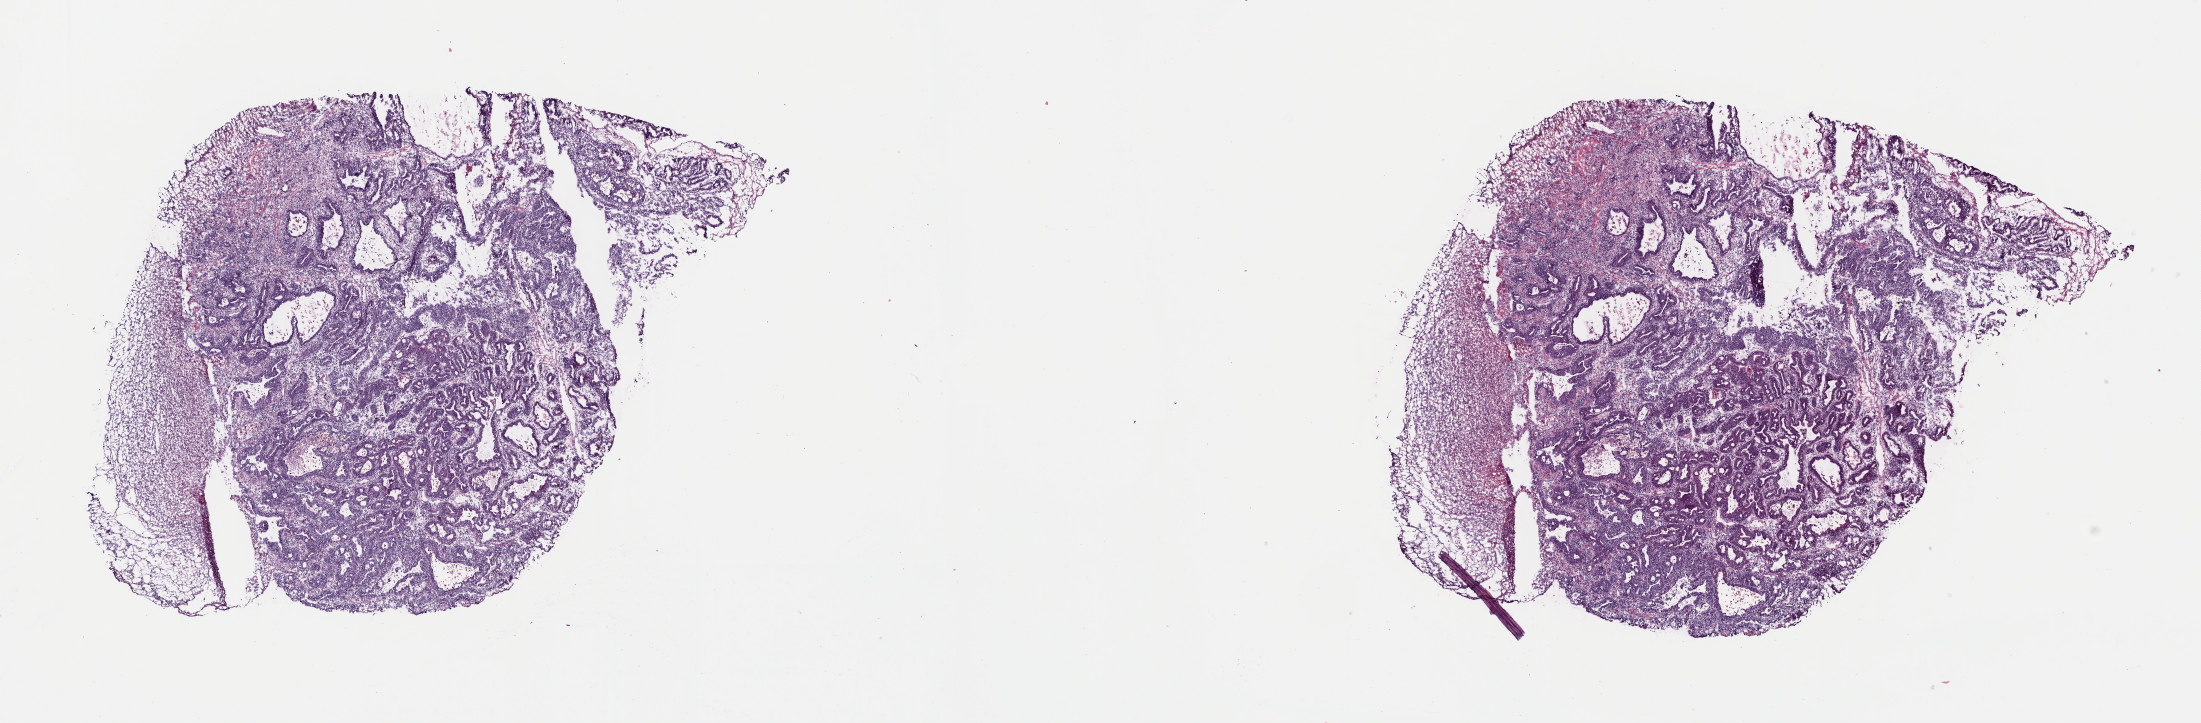
Whole-slide histology image, H&E — low-resolution overview of the scanned area, about 17.4 x 5.7 mm (acquisition: 40x scan), frozen section, primary tumour sample from the esophagus. Female patient; age at initial diagnosis 67 years. Histologic grade: G2 (moderately differentiated). Pathologist review of this section (percent, as recorded): tumour cells 100%, tumour nuclei 65%, normal cells 0%, stromal cells 0%, necrosis 0%. Infiltration values recorded for this section: lymphocyte infiltration 6%, monocyte infiltration 1%, neutrophil infiltration 2%.
Pathologic diagnosis: Adenocarcinoma, NOS (lower third of esophagus). AJCC pathologic stage: IA (7th edition).